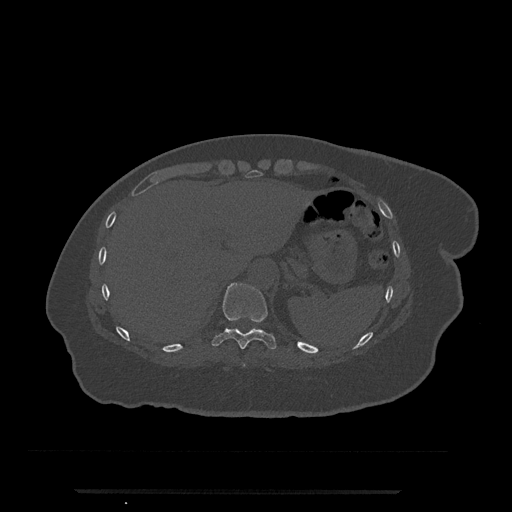
CT including the spine, one axial slice. Slice 283 of 797 in the series (ordered by position). Bone window (W 1800 / L 400 HU). 0.5 mm slice thickness. 512 × 512 image matrix. Female patient, age 51 years. Case-level facts recorded for this patient, not image findings: primary cancer: neuro; vertebrae with lytic lesions (as recorded): T8.
Annotated regions visible in this slice (semi-automatically segmented with operator editing):
- T10 vertebra: bounding box (x1, y1, x2, y2) in pixels: (212, 282, 277, 350)
- T9 vertebra: (243, 363, 246, 367)